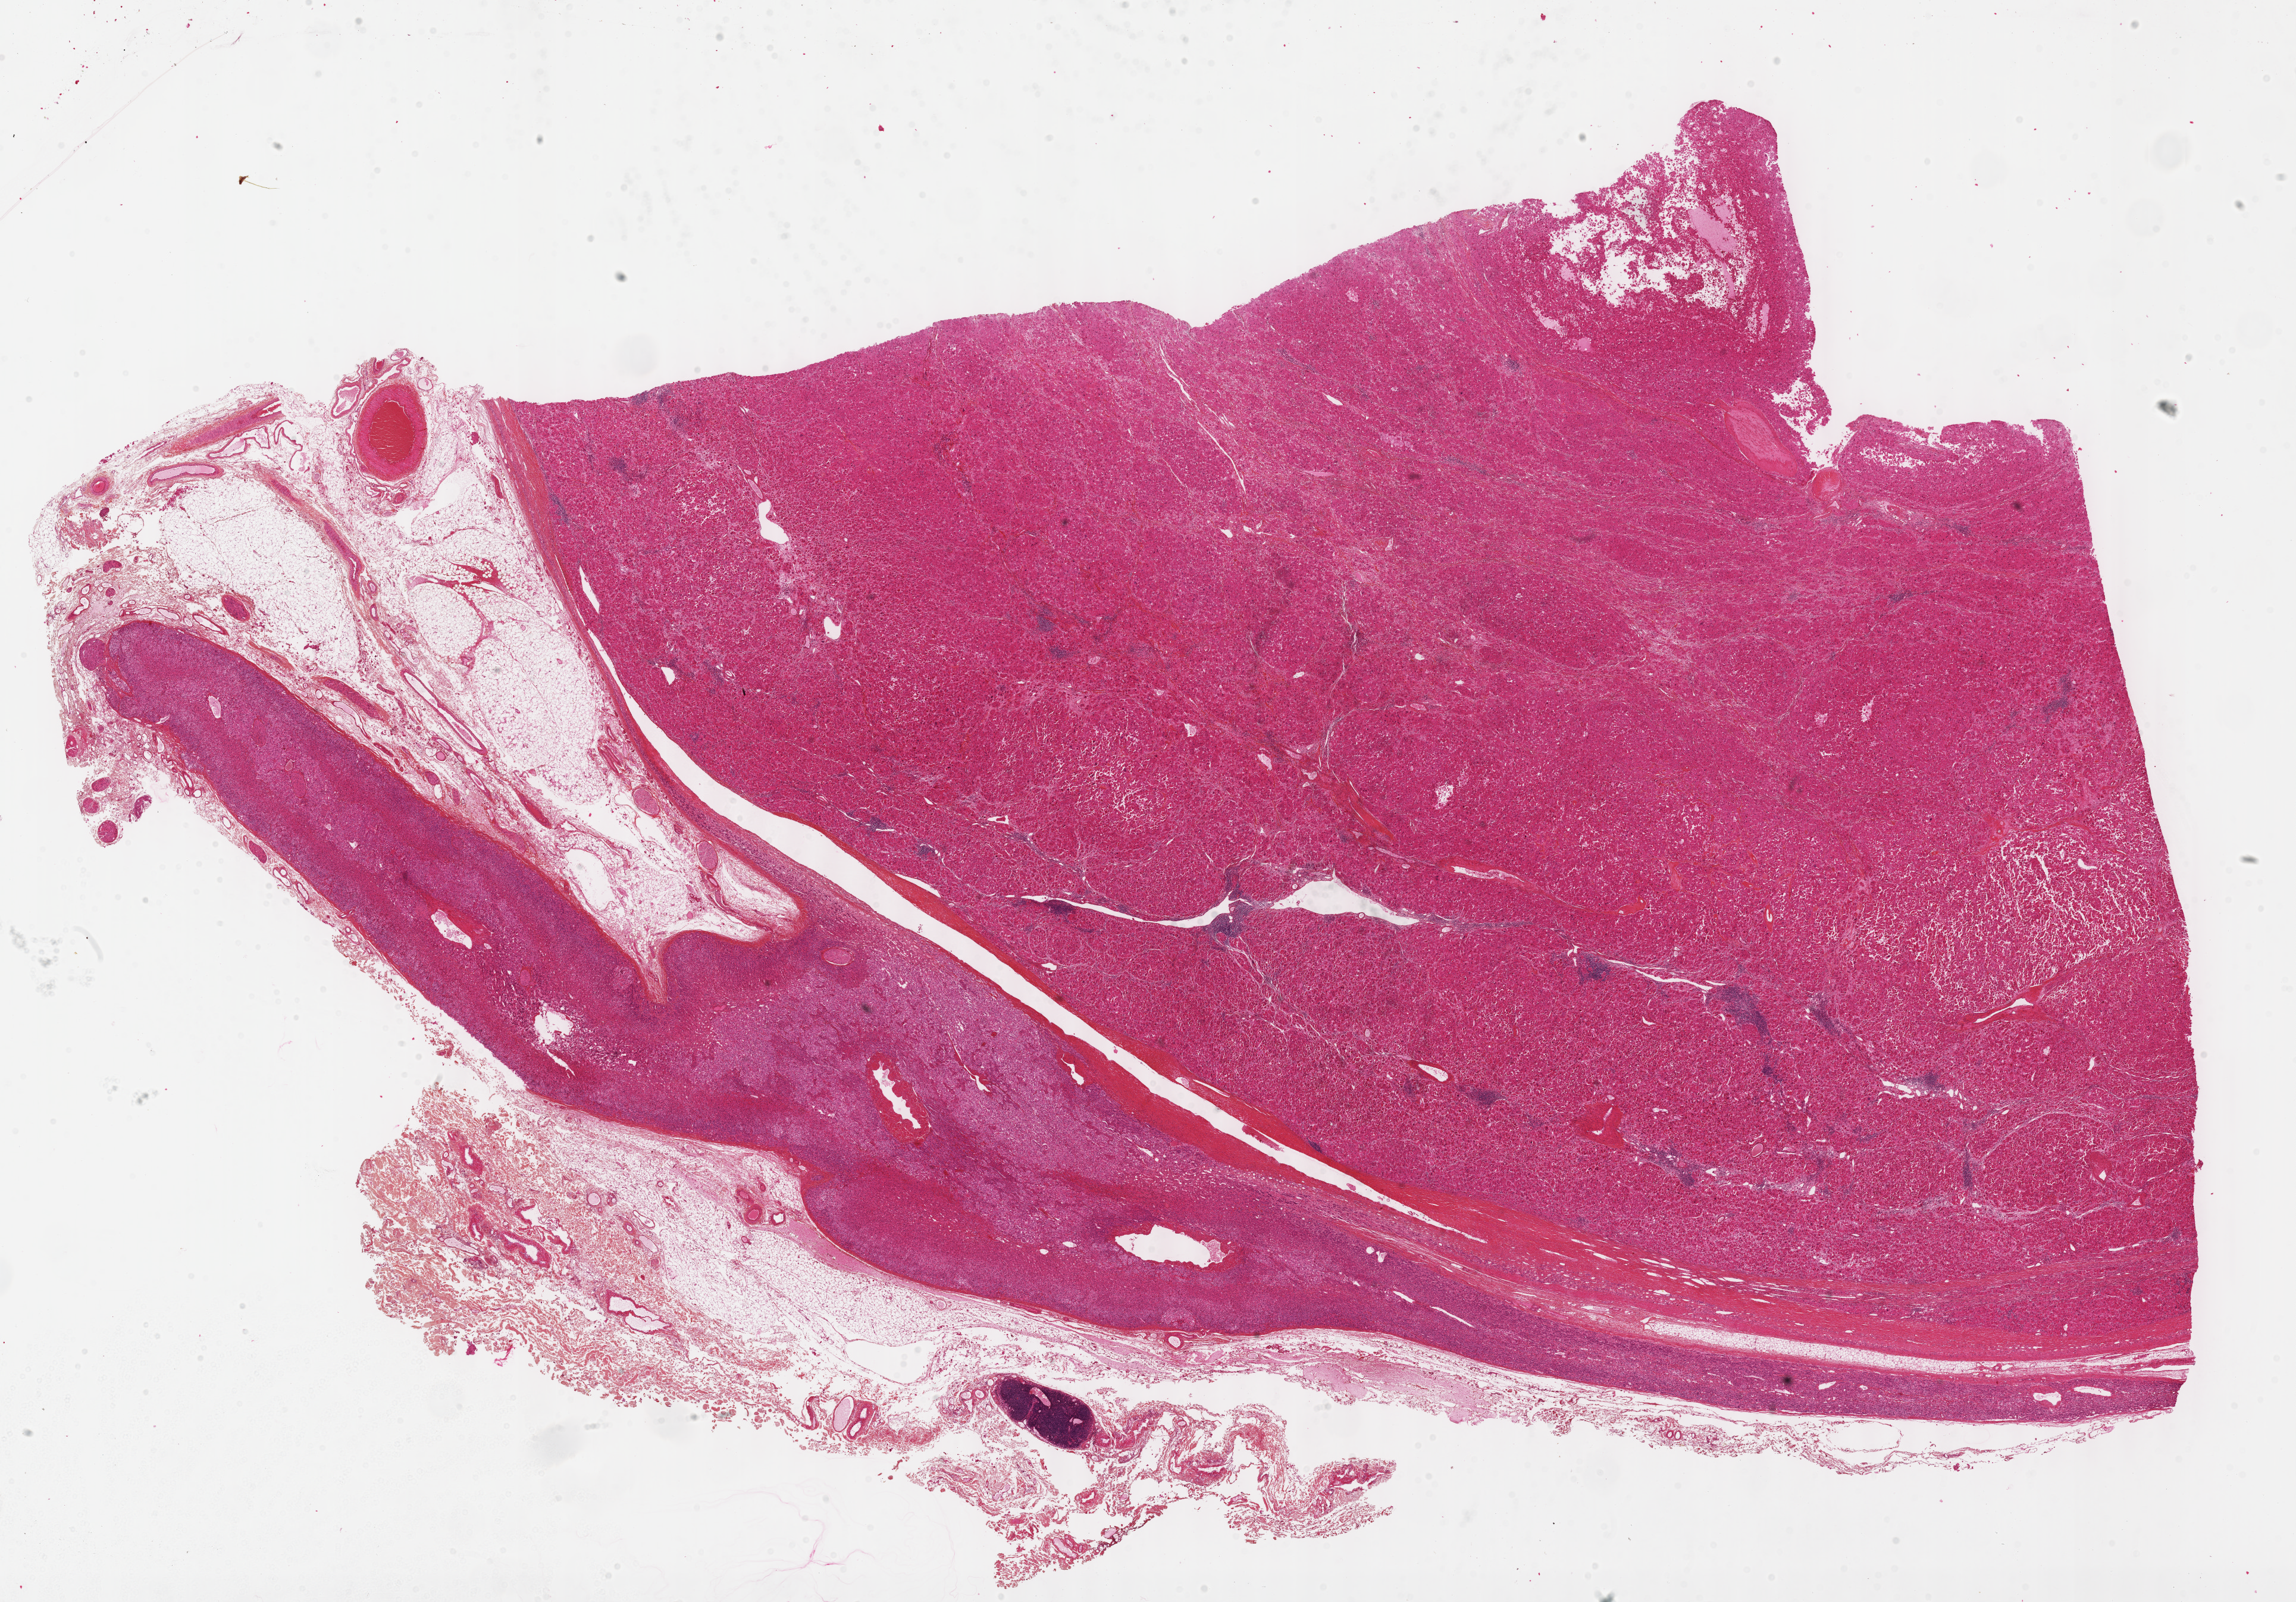
Whole-slide histology image, H&E, whole scanned area (about 31.2 x 21.8 mm) shown as a low-resolution overview, formalin-fixed paraffin-embedded (FFPE) diagnostic section, sample: primary tumour, adrenal cortex. Patient: female, age at initial diagnosis 37 years.
• diagnosis: Adrenal cortical carcinoma
• laterality: right